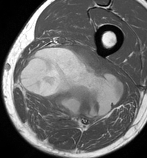
MRI of an extremity soft-tissue mass, one axial slice. Slice 45 of 86 in the series (ordered by position). MR volume resampled by the dataset authors to the PET/CT grid (not the native acquisition matrix). 3.27 mm slice thickness. 147 × 158 image matrix, field of view 144 × 154 mm. Male patient. From the clinical record (not read from this slice): histological type: undifferentiated pleomorphic liposarcoma; grade: high; site of the primary tumour: left thigh.
Outlined on this slice (expert contour drawn on MRI and transferred to this co-registered scan by the dataset authors):
- gross tumour volume including surrounding oedema: box from (x=18, y=46) to (x=124, y=130) px
- gross tumour volume (mass): (x=19, y=46)–(x=124, y=130)